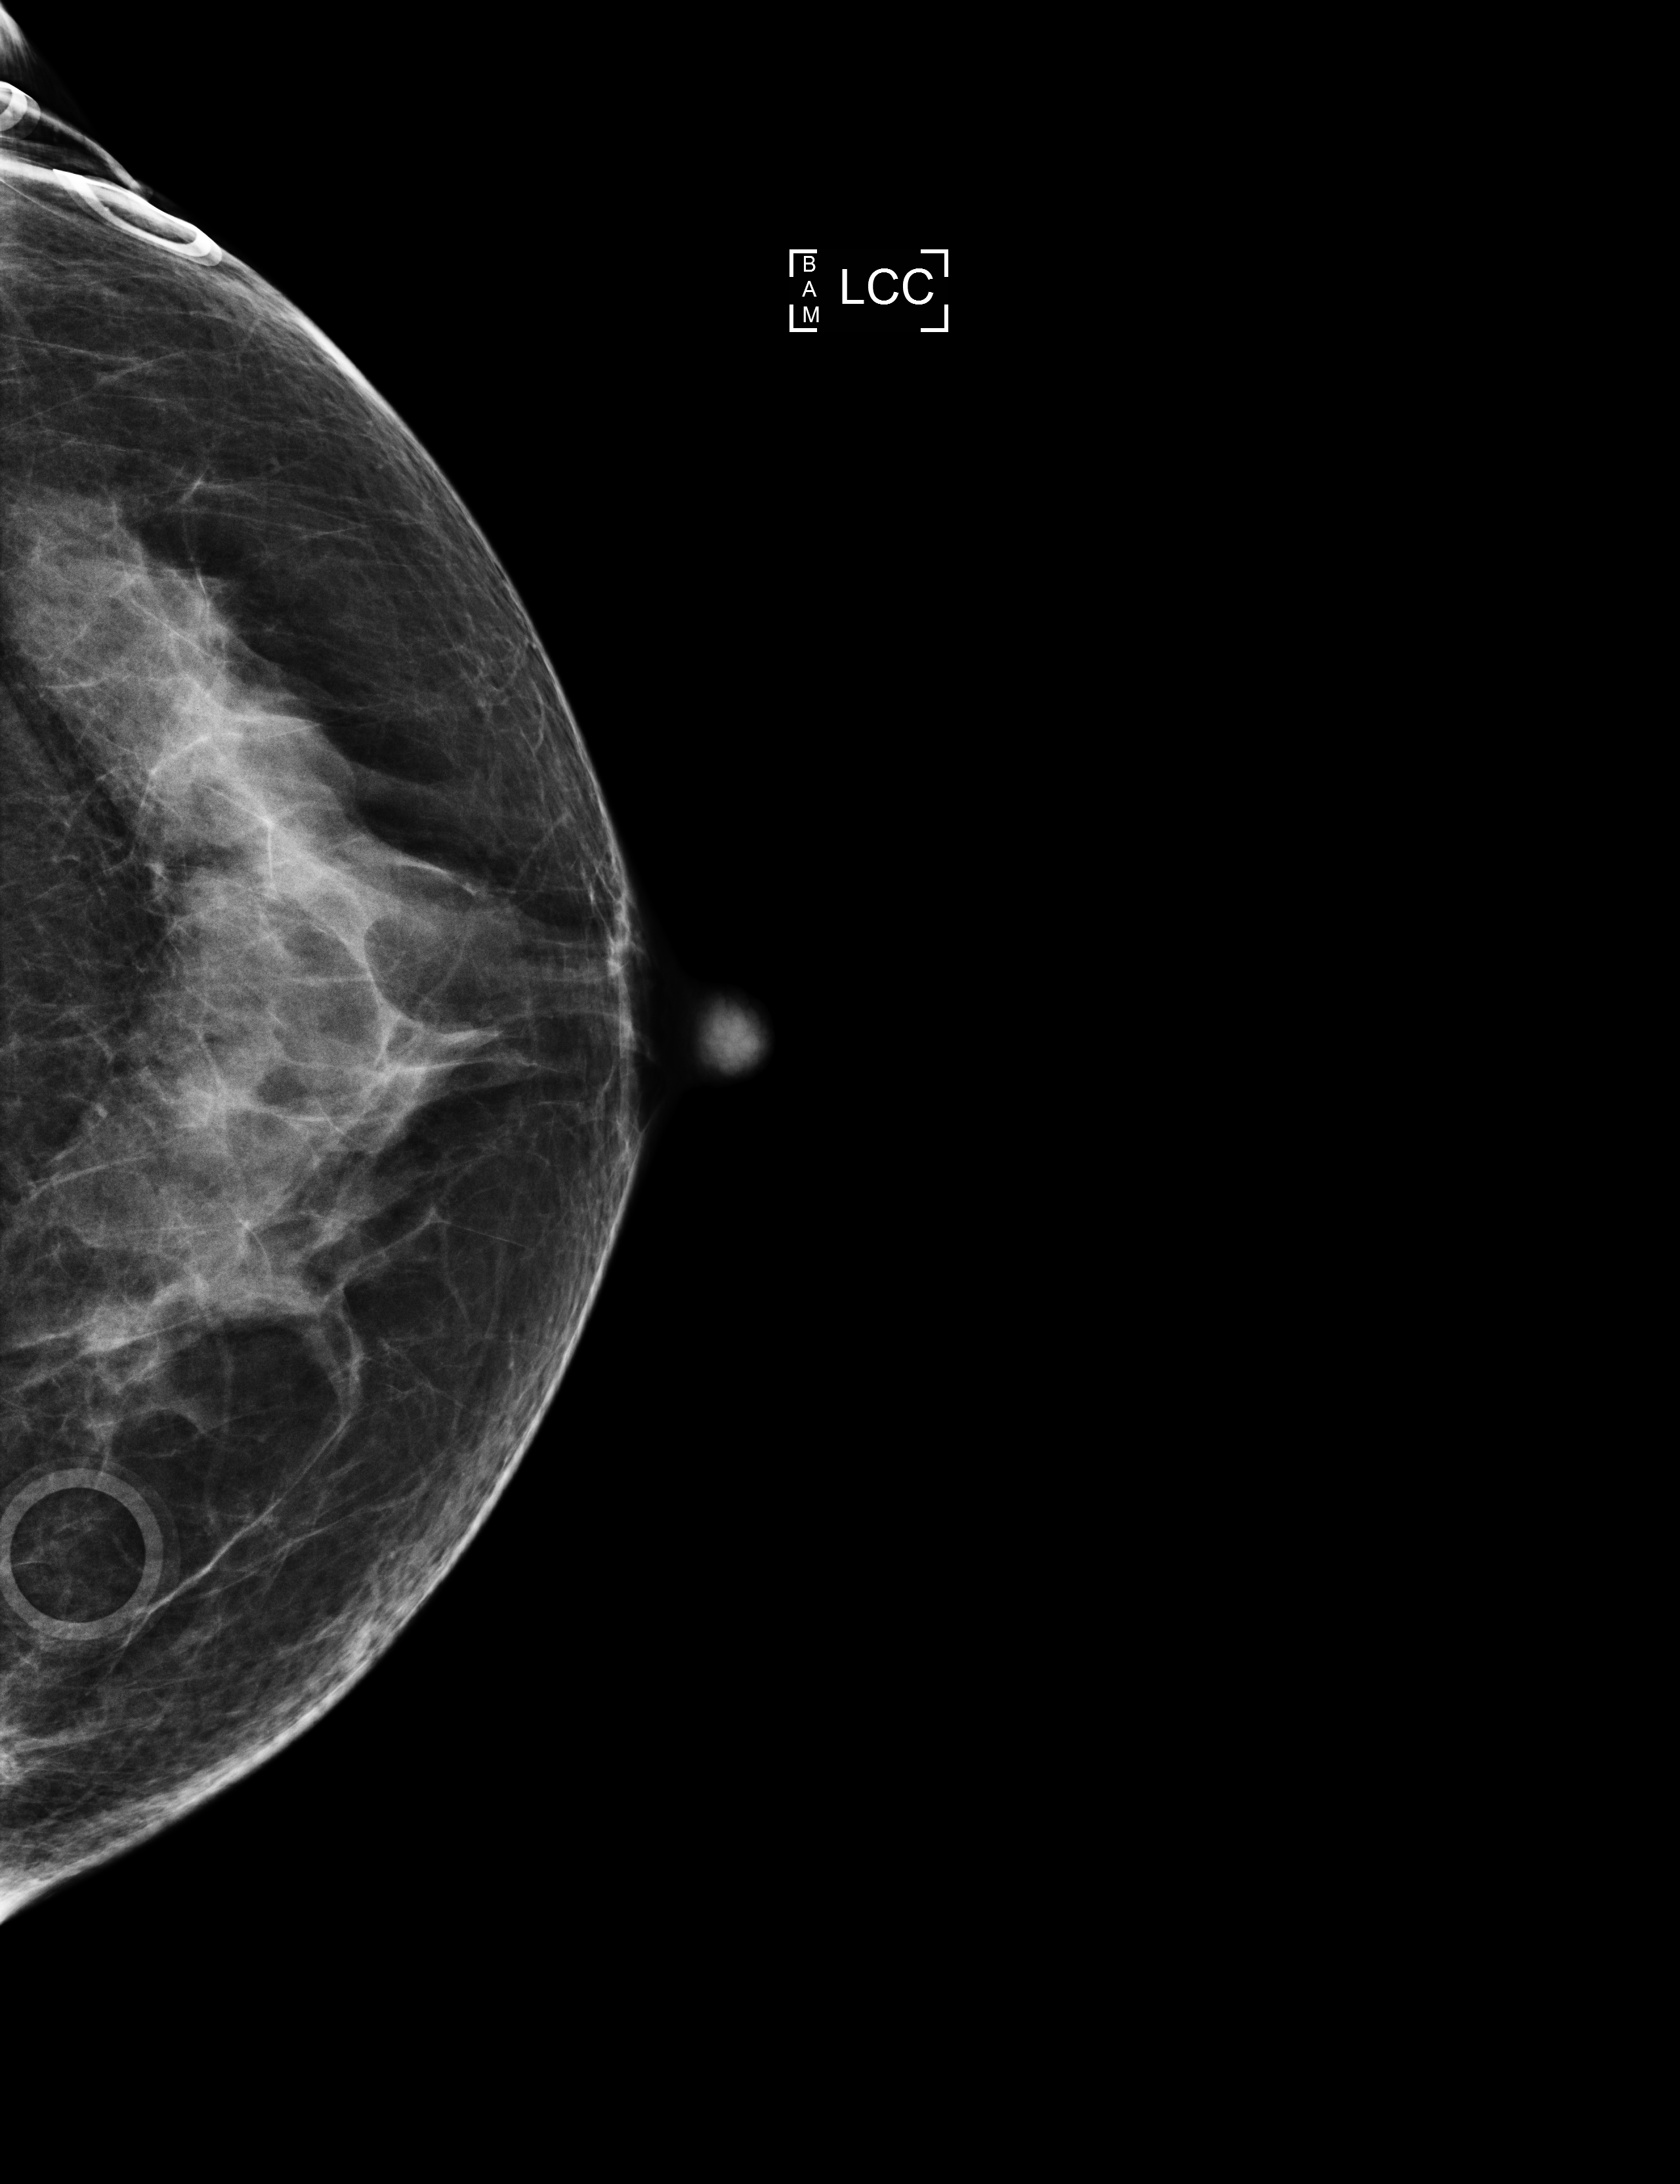
Full-field digital mammogram (FFDM); left breast; cranio-caudal projection; screening examination; compressed breast thickness 65 mm. Female patient, age 59 years.
BI-RADS breast density category at the screening exam (both breasts, scale 1–4): 3. Final BI-RADS category for the screening round (tomosynthesis exam, both breasts): category 1. Recall: no recall after this screen.